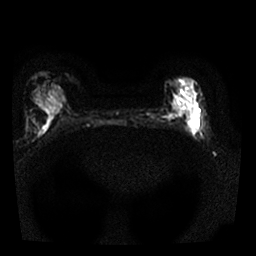
Breast MRI, one axial slice. Position 12 of 25 along the scan axis. Diffusion-weighted series; image 2 of 4 stored at this slice position (different b-values; order by instance number). 1.5 T. 4 mm slice thickness. 256 × 256 image matrix. Female patient.
Annotated regions visible in this slice (manually delineated by an expert):
- tumour on diffusion-weighted imaging: bounding box <190,113,196,136> (left, top, right, bottom; pixels)